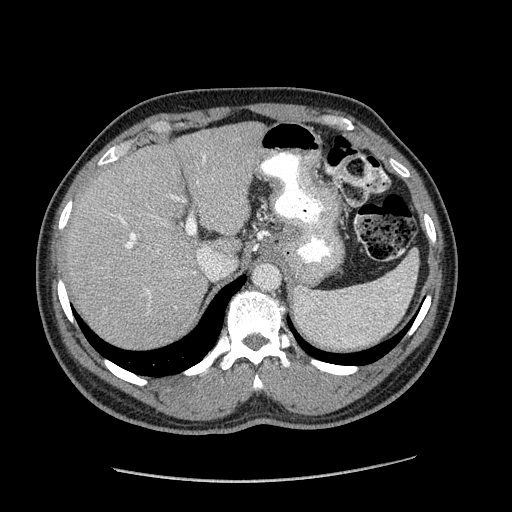
Contrast-enhanced abdominal CT (liver protocol), one axial slice. Position 131 of 182 along the scan axis. Reconstruction kernel STANDARD. Soft-tissue window (W 400 / L 40 HU). 2.5 mm slice thickness. 512 × 512 image matrix, field of view 400 × 400 mm. From the clinical record (not read from this slice): diagnosis: hepatocellular carcinoma (patient treated with transarterial chemoembolisation; whether this scan precedes or follows treatment is not stated here); TNM stage (as recorded): Stage-I; Child-Pugh class: A; tumour differentiation: well differentiated; tumour nodularity: uninodular.
Outlined on this slice (semi-automatic segmentation, software-assisted and operator-edited):
- liver parenchyma outside the tumour (the mass and vessels are separate outlines, so this box may not span the whole liver): bounding box [x1, y1, x2, y2] px = [63, 122, 264, 346]
- liver vessels: [118, 156, 206, 292]